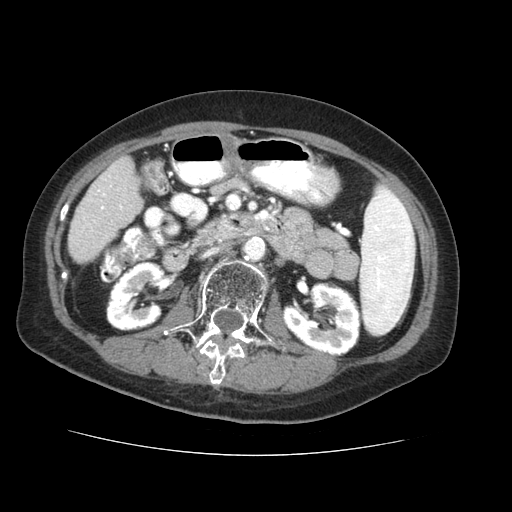
Contrast-enhanced abdominal CT (liver protocol), one axial slice; slice 11 of 73 in the series (ordered by position); reconstruction kernel STANDARD; soft-tissue window (W 400 / L 40 HU); 2.5 mm slice thickness; 512 × 512 image matrix, field of view 360 × 360 mm. From the clinical record (not read from this slice): diagnosis: hepatocellular carcinoma (patient treated with transarterial chemoembolisation; whether this scan precedes or follows treatment is not stated here); TNM stage (as recorded): Stage-IVB; Child-Pugh class: A; tumour differentiation: well differentiated.
Annotated regions visible in this slice (semi-automatic segmentation, software-assisted and operator-edited):
- liver parenchyma outside the tumour (the mass and vessels are separate outlines, so this box may not span the whole liver): bounding box <74,156,140,260> (left, top, right, bottom; pixels)